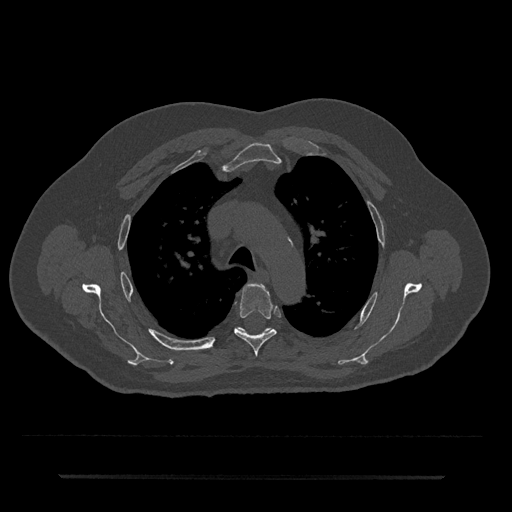
CT including the spine, one axial slice. Slice 522 of 797 in the series (ordered by position). Reconstruction kernel Br40s/3. 120 kVp. Bone window (W 1800 / L 400 HU). 512 × 512 image matrix. Male patient, age 69 years. Case-level facts recorded for this patient, not image findings: primary cancer: prostate.
Annotated regions visible in this slice (semi-automatic segmentation, software-assisted and operator-edited):
- T4 vertebra: bounding box <234,283,277,357> (left, top, right, bottom; pixels)
- T5 vertebra: <237,327,273,333>